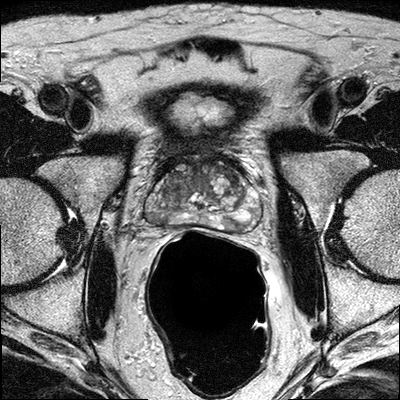
MRI of the prostate; 3 images, each a single mid-volume slice chosen by position (not for content). Treatment context recorded for this patient: Surgery.
Image 1: T2-weighted axial slice, series "T2W_TSE_AX", slice 17 of 32, 3 mm slice thickness.
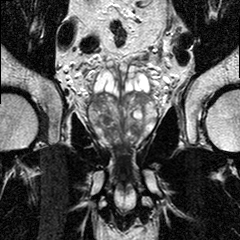
Image 2: T2-weighted coronal slice, series "T2W_TSE_COR", slice 15 of 28.
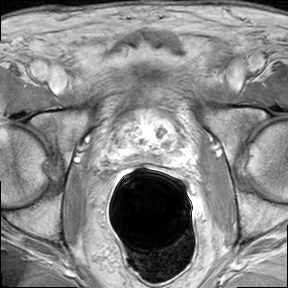
Image 3: axial dynamic contrast-enhanced (DCE) T1-weighted image, slice 17 of 32, dynamic phase 5 of 8, 6 mm slice thickness.
Report of this MRI examination:
Indication: patient with Gleason 8 prostate cancer; PSA 15; Preoperative assessment for extraglandular extension and staging.
FINDINGS: The prostate has a maximal lateral diameter of 4.8 cm, a maximal craniocaudal diameter of 3.8 cm and a maximal AP diameter of 2.9 cm resulting in an estimated gland volume of 28 cc. The zonal anatomy is preserved. Within the midthird of the prostate, with extension into the apical third on the left and right and left prostate base, in left and right posteriorly lateral peripheral zones, there areas of irregular, geographic T-2 weighted high pole intense signal seen, which show along the dynamic contrast-enhanced series suspicious enhancement was rapid wash in and wash out pattern, especially on the right side, the enhancement pattern is suspicious for more aggressive tumor. The left side however shows suspicious enhancement, too. The dominant nodule on the right side measures 15 x 9 mm on the left side 12 x 7 mm. Capsular infiltration on the right is possible. No manifest extraglandular disease on either side. No evidence for involvement of the neurovascular bundle on either side. No evidence for seminal vesicles infiltration. No evidence of involvement of bladder neck and rectal wall. No suspiciously enlarged obturator and iliac lymph nodes. Multiplanar reconstructions, subtraction images, and CAD analysis of the dynamic series for assessment of the kinetic information facilitated the interpretation of the exam.
IMPRESSION: 1) Findings suggestive for bilateral cancer in the left and right peripheral zones of right and left base, right and left midthird, and left apical third, as detailed above. 2) No evidence of definite extracapsular disease on either side. Neurovascular bundles and seminal vesicles uninvolved. 3) No local/pelvic lymphadenopathy (up to the aortic bifurcation).

Prostate biopsy pathology (as recorded):
Specimen consists of multiple core fragments of tan soft tissue measuring 0.5cm to 1.7cm in length and 0.1cm in diameter. The specimen is submitted entirely in six cassettes.1-right pz, 2-right pz/tz, 3-right apex, 4-left pz, 5-left pz/tz, 6-left apex. 1. RIGHT PZ:
PROSTATIC ADENOCARCINOMA, GLEASON SCORE 4+3=7/10, INVOLVING 80% OF THE TISSUE REPRESENTED. 2. RIGHT PZ/TZ: PROSTATIC ADENOCARCINOMA, GLEASON SCORE 4+4=8/10, INVOLVING 60% OF THE TISSUE REPRESENTED. 3. RIGHT APEX: BENIGN PROSTATIC TISSUE, NO TUMOR IDENTIFIED. 4. LEFT PZ: BENIGN PROSTATIC TISSUE, NO TUMOR IDENTIFIED.
5. LEFT PZ/TZ: PROSTATIC ADENOCARCINOMA, GLEASON SCORE 3+3=6/10, INVOLVING 40% OF THE TISSUE REPRESENTED. 6. LEFT APEX: PROSTATIC ADENOCARCINOMA, GLEASON SCORE 3+3=6/10, INVOLVING 20% OF THE TISSUE REPRESENTED. NOTE: PERINEURAL INVASION IS PRESENT.

Prostatectomy specimen pathology (as recorded; the surgery followed this MRI):
Specimen is received fresh and fixed in five containers labeled with the patient name, hospital number and A. Right Pelvic Lymph Nodes, B. Left Pelvic Lymph Nodes, C. Bladder Neck Tissue, D. Left Pedicle and E. Prostate And Seminal Vesicle. Specimen A consists of multiple fragments of yellow fatty tissue measuring 3x3x0.5cm in aggregate with potential lymph nodes measuring from 0.3 to 0.6cm. The specimen is submitted entirely in two cassettes labeled A1 and A2. Specimen B consists of multiple fragments of yellow fatty tissue measuring 2.2x2x0.7cm in aggregate with two potential lymph nodes measuring 0.8 and 0.9cm. The two lymph nodes are submitted in cassette B1 and the remaining fatty tissue submitted in cassette B2. Specimen C consists of a small fragment of brown soft tissue measuring 0.5x0.2x0.2cm. Specimen is submitted entirely in one cassette labeled C.
Specimen D consists of a small fragment of tan soft tissue measuring 0.8x0.4x0.2cm. Specimen is submitted entirely in a single cassette labeledD. Specimen E consists of a prostatectomy specimen with attached vas deferens and seminal vesicles weighing 61.1 grams and measuring 4.5x3.4x3.2cm. The right seminal vesicle measures 4x1.8x0.6cm, the left seminal vesicle measures 3.5x1.5x0.5cm. The right vas deferens measures 3.5cm in length x0.3cm in diameter and the left vas deferens measures 3cm in length x0.4cm in diameter. The prostate appears symmetrical and the surface appears intact. The right side is inked black and the left side is inked blue. It is serially sectioned to reveal a distinct yellowish / white nodule in the right posterior lobe measuring 1.2x1x0.9cm. The rest of the parenchyma is somewhat nodular however there are no more distinct nodules identified. The specimen is submitted entirely as follows: cassette E1; vas deferens tips, E2; left urethral margin, radially sectioned, E3; right urethral margin, radially sectioned, E4; left bladder neck margin, radially sectioned, E5; right bladder neck margin, radially sectioned, E6 through E13; right anterior lobe, sectioned from apex to base, E14 through E22; right posterior lobe sectioned from apex to base with the seminal vesicle submitted in cassette E22, E23 through E29; left anterior lobe, sectioned from apex to base, E30 through E37; left posterior lobe sectioned from apex to base with the seminal vesicle submitted in cassette E37.
Final Diagnosis A. RIGHT PELVIC LYMPH NODES:SIX (6) REACTIVE LYMPH NODES. NO TUMOR IDENTIFIED. B. LEFT PELVIC LYMPH NODES:SIX (6) REACTIVE LYMPH NODES. NO TUMOR IDENTIFIED. C. BLADDER NECK TISSUE: FRAGMENT OF FIBROCONNECTIVE TISSUE.NO TUMOR IDENTIFIED.
D. LEFT PEDICLE:FRAGMENT OF FIBROCONNECTIVE TISSUE. NO TUMOR IDENTIFIED. E. PROSTATE AND SEMINAL VESICLE: Procedure: Radical prostatectomy Prostate Size: 4.5X3.4X3.2 cm Weight: 61.1g Lymph Node Sampling: Pelvic lymph node dissection Histologic Type: Adenocarcinoma (acinar, not otherwise specified) Histologic Grade: Gleason grade 4+3 score = 7/10 Primary pattern: Grade 4 Secondary pattern: Grade 3 Tumor Quantitation: Proportion (percentage) of prostate involved by tumor: 15% Extraprostatic Extension: Not identified Seminal Vesicle Invasion: Not identified Margins: Margins uninvolved by invasive carcinoma Treatment Effect on Carcinoma: Not identified Lymph-Vascular Invasion: Not identified Perineural Invasion: Present Additional Pathologic Findings: High-grade prostatic intraepithelial neoplasia (PIN) and chronic inflammation Pathologic Staging (pTNM) : Primary Tumor (pT) pT2c: Bilateral disease Regional Lymph Nodes (pN) pN0: No regional lymph node metastasis Specify: Number examined: 12 Number involved: 0 Distant Metastasis (pM: Not applicable AJCC Pathologic Stage: (pT2c, pN0)
Clinical diagnosis and History: 72 year old male with Prostate cancer.